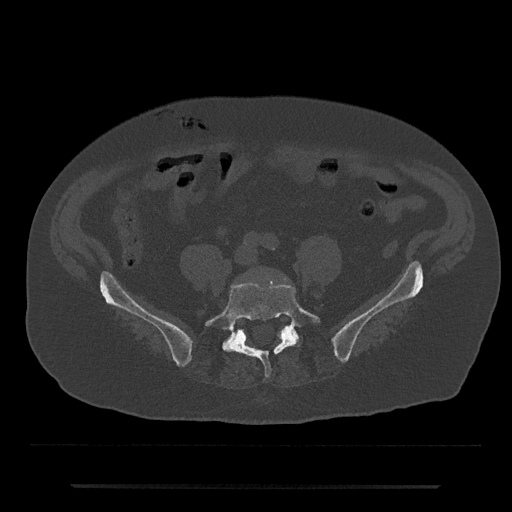
CT including the spine, one axial slice. Position 288 of 797 along the scan axis. Reconstruction kernel Br40s/3. Bone window (W 1800 / L 400 HU). 0.5 mm slice thickness. 512 × 512 image matrix. Male patient, age 80 years. Case-level facts recorded for this patient, not image findings: primary cancer: prostate; vertebrae with lytic lesions (as recorded): L1, T11.
Annotated regions visible in this slice (semi-automatic segmentation, software-assisted and operator-edited):
- L5 vertebra: bounding box [x1, y1, x2, y2] px = [204, 283, 320, 377]